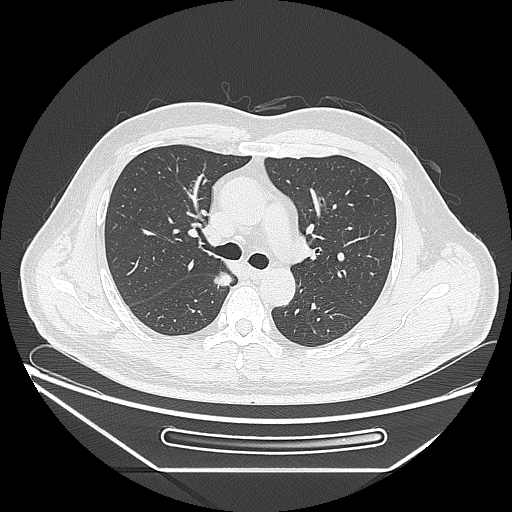
Chest CT, one axial slice. Slice 164 of 271 in the series (ordered by position). Reconstruction kernel LUNG. Lung window (W 1500 / L -600 HU). 512 × 512 image matrix. Patient: male, 49 years. Case-level facts recorded for this patient, not image findings: clinical TNM (as recorded): T1b N0 M0.
Annotated regions visible in this slice (rectangle marked by the reading radiologist):
- lung tumour (recorded histology: adenocarcinoma): bounding box <208,267,237,297> (left, top, right, bottom; pixels)